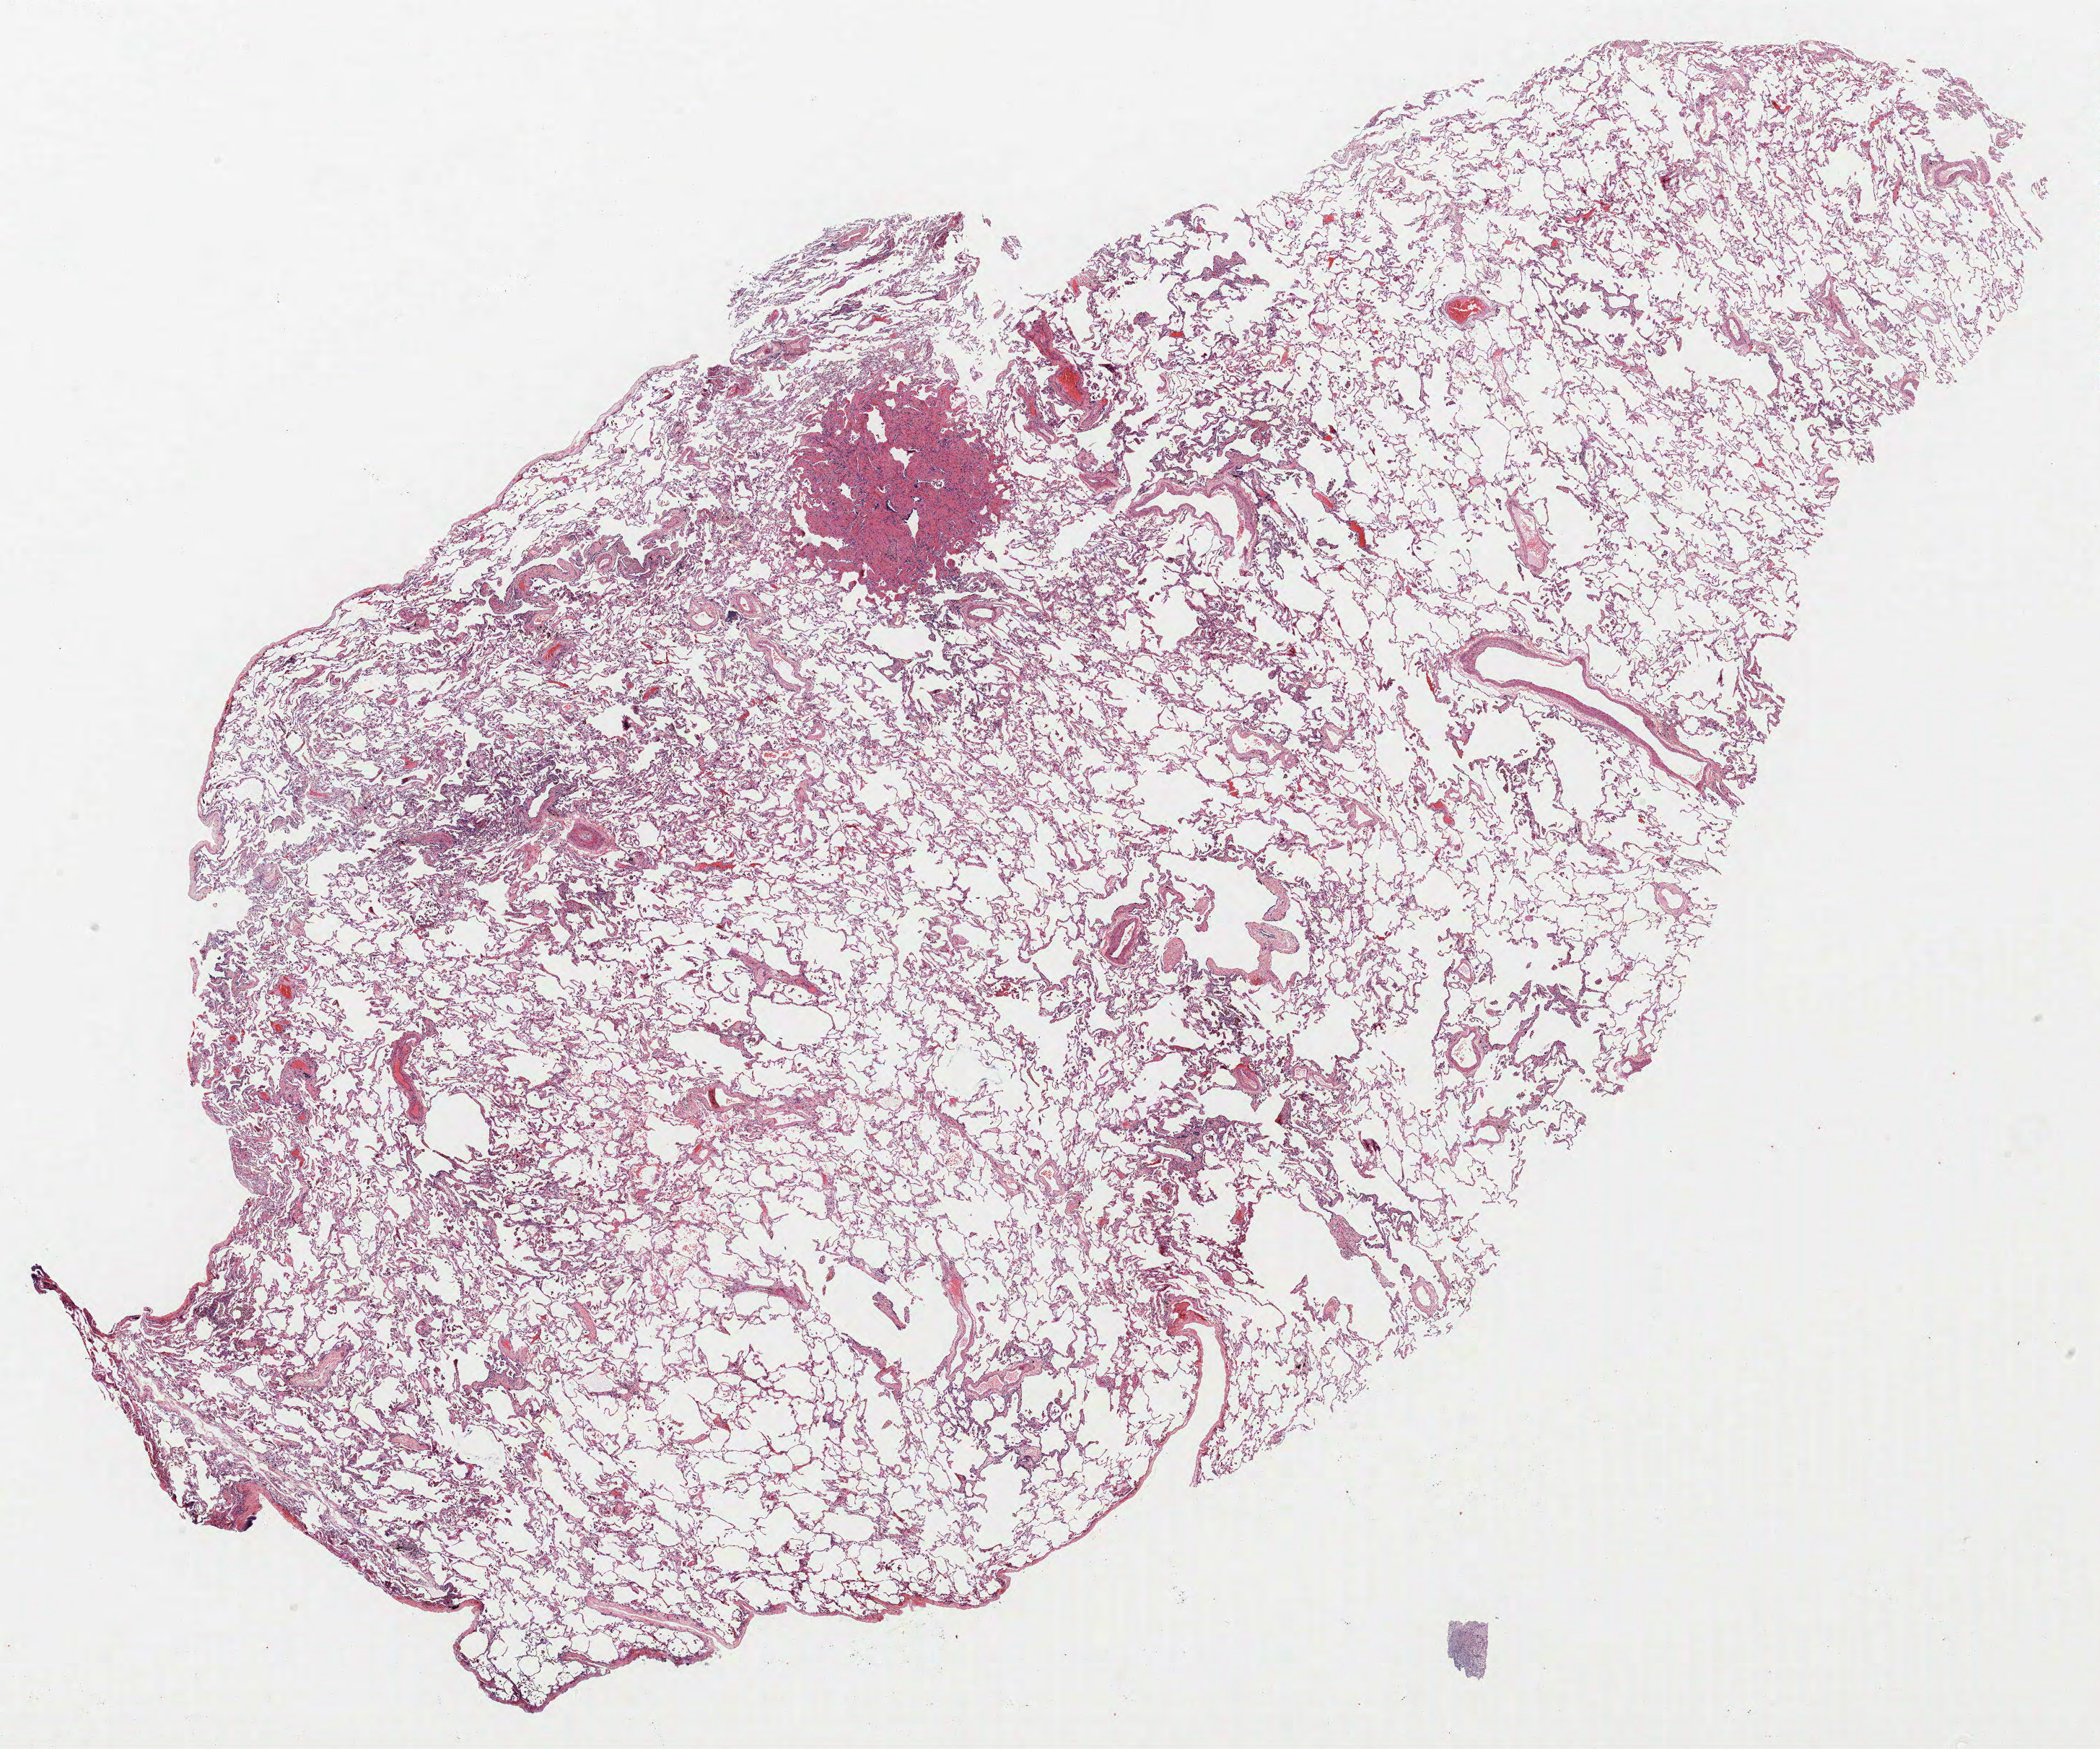
H&E-stained whole-slide image, a low-resolution overview of the entire scanned area, about 23.3 x 19.4 mm (acquisition: 40x scan); FFPE section; lung. Female, age 59 at enrolment. Grade: poorly differentiated (G3).
Stage (AJCC 6th edition): IA. Primary tumour location (clinical record): left upper lobe. Participant's lung-cancer diagnosis: Large cell neuroendocrine carcinoma. Tumour size (pathology): 12 mm.